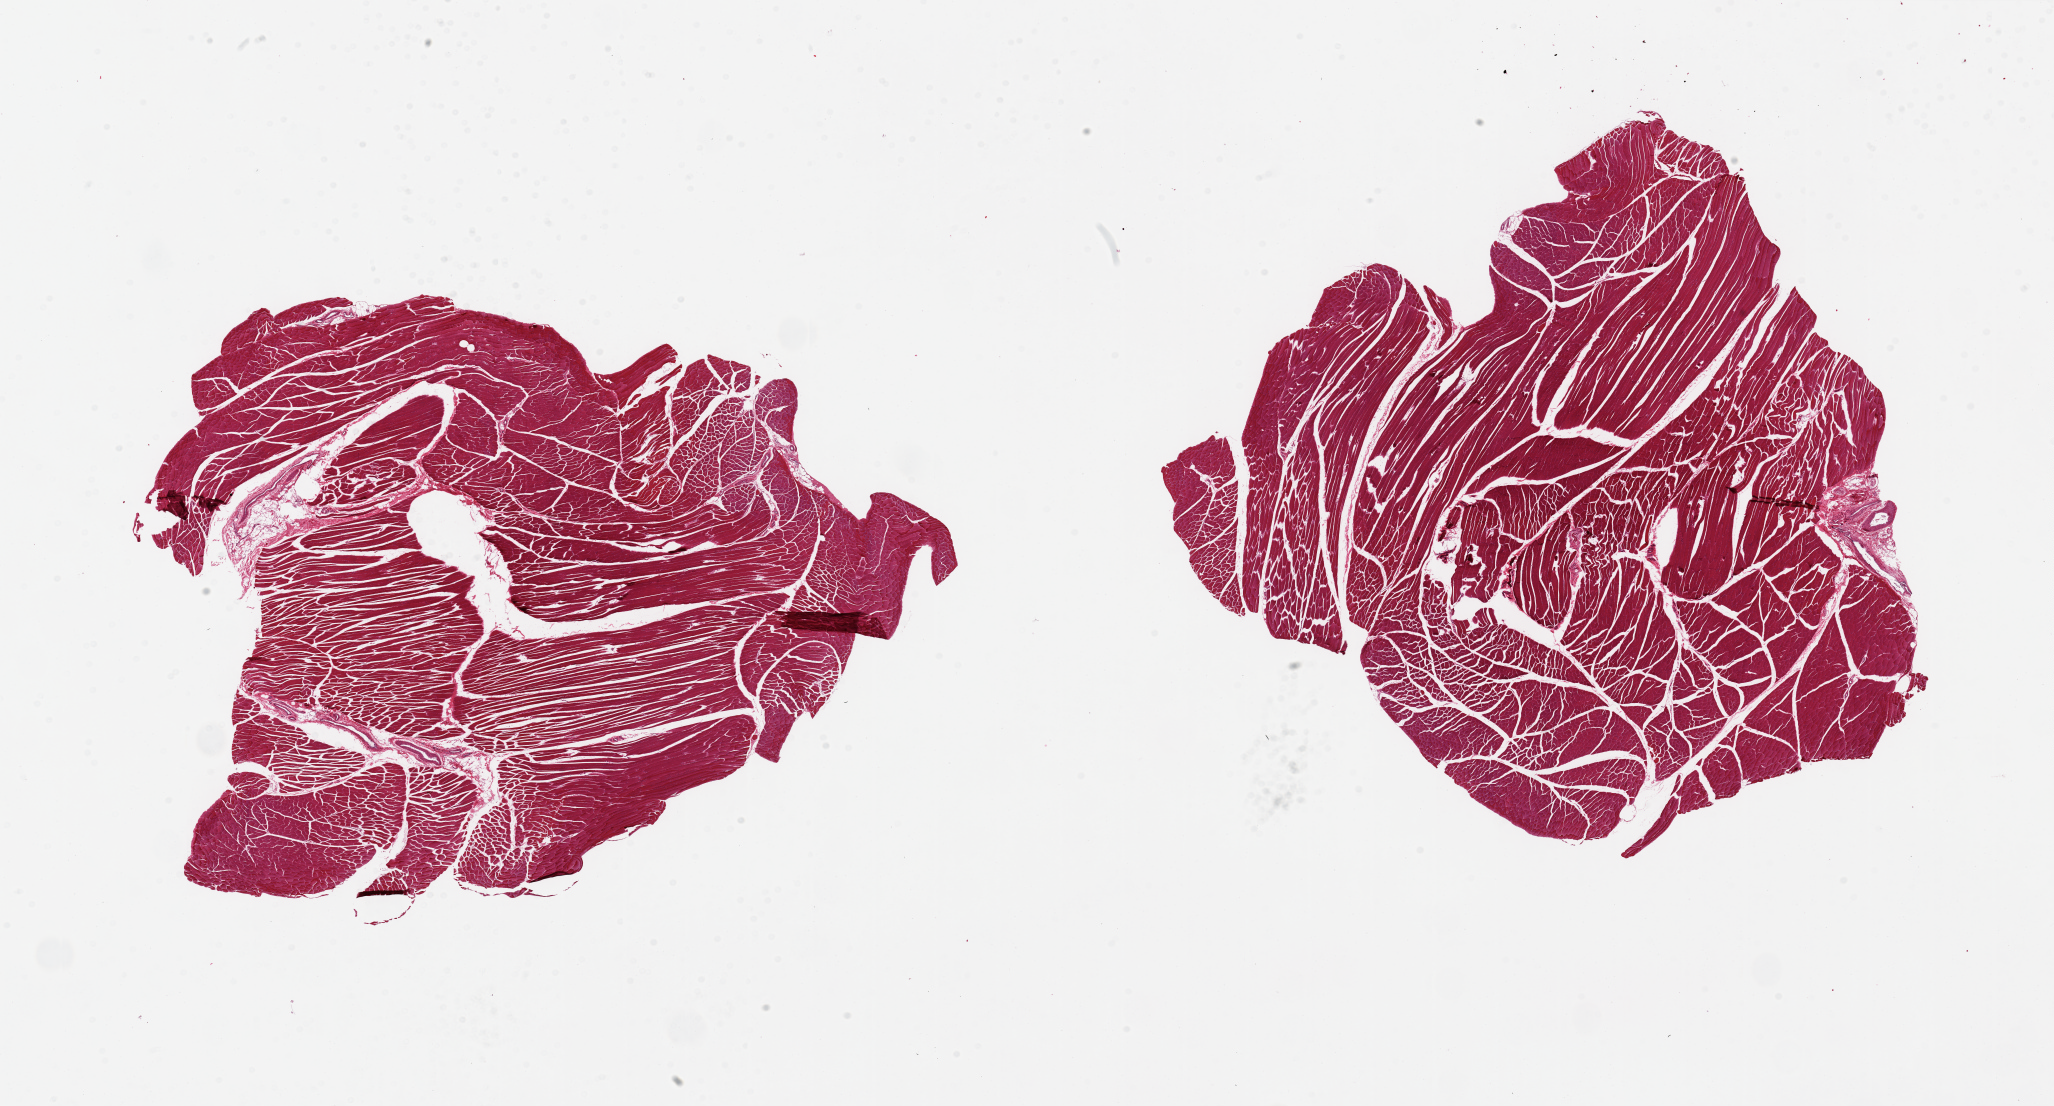
Digitized haematoxylin and eosin-stained section, brightfield, whole scanned area (about 32.5 x 17.5 mm, acquisition: 20x scan) shown as a low-resolution overview, PAXgene-fixed, paraffin-embedded tissue, section of skeletal muscle (target tissue), tissue donor sample. Donor sex: male.
Reviewer comment on this tissue sample: 2 pieces; no extraneous tissue.